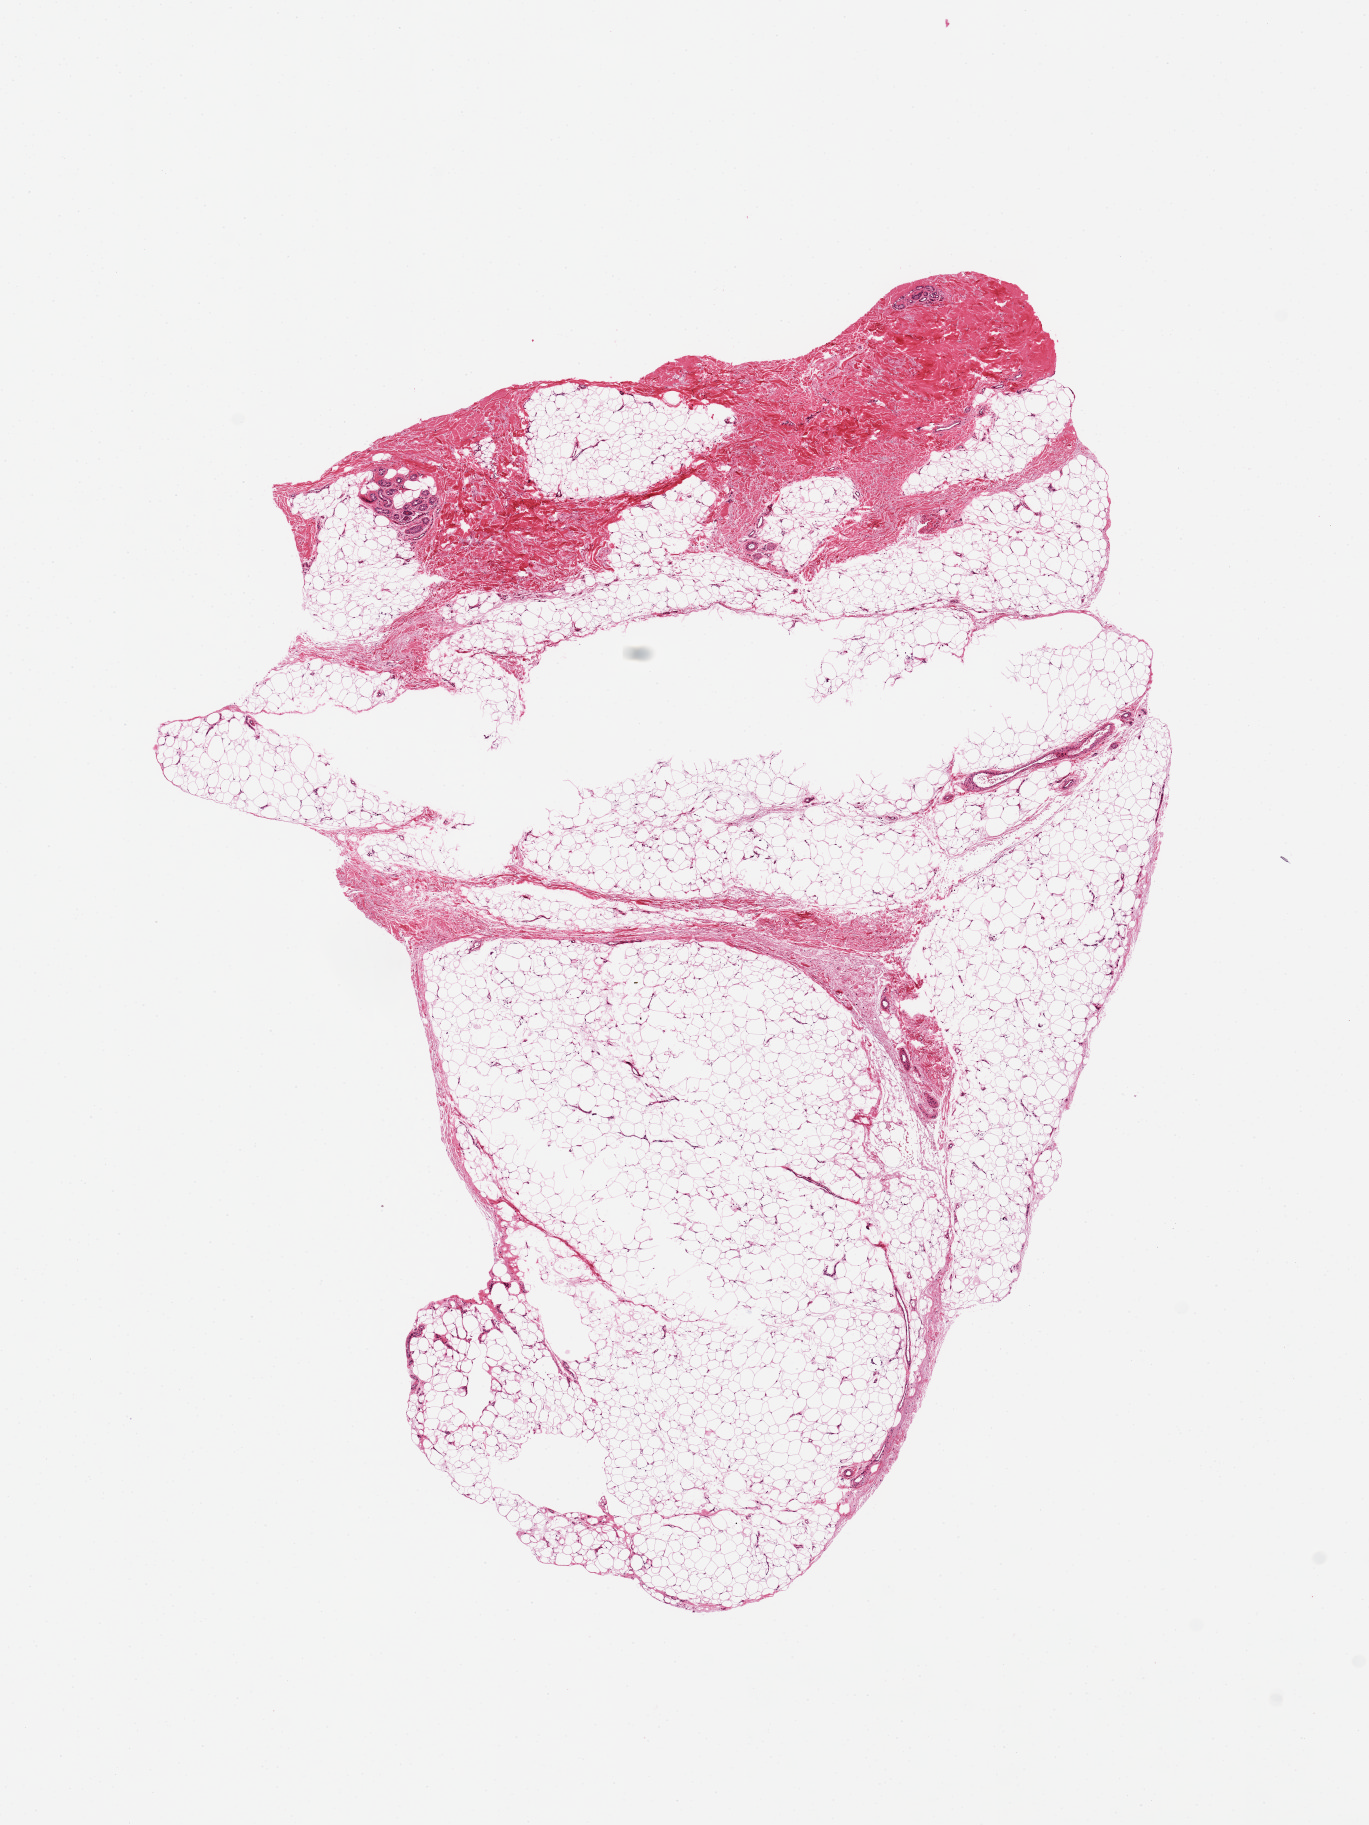
Whole-slide image, haematoxylin and eosin stain, brightfield, low-resolution overview of the scanned area, about 10.8 x 14.4 mm (from a 20x scan). PAXgene-fixed, paraffin-embedded tissue. Section of adipose tissue (target tissue). Donor tissue sample. Donor sex: male.
- reviewer comment on this tissue sample: slight underfixation centrally